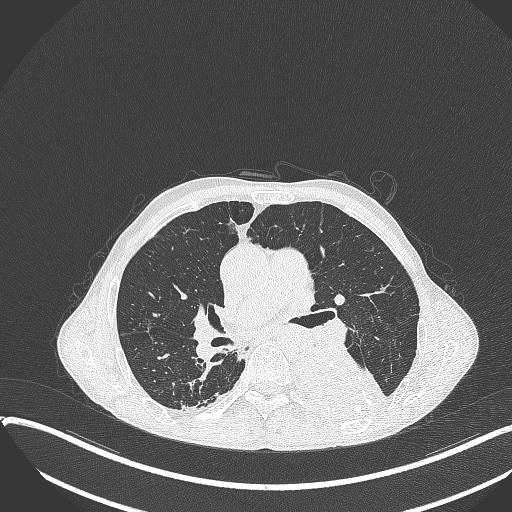
Chest CT, one axial slice; slice 216 of 401 in the series (ordered by position); reconstruction kernel B70f; 120 kVp; lung window (W 1500 / L -600 HU); 1 mm slice thickness; 512 × 512 image matrix, field of view 400 × 400 mm. Male patient, age 57 years. From the clinical record (not read from this slice): clinical TNM (as recorded): T4 N0 M0.
Annotated regions visible in this slice (bounding box drawn by a radiologist):
- lung tumour (recorded histology: squamous cell carcinoma): bounding box [x1, y1, x2, y2] px = [288, 349, 387, 422]